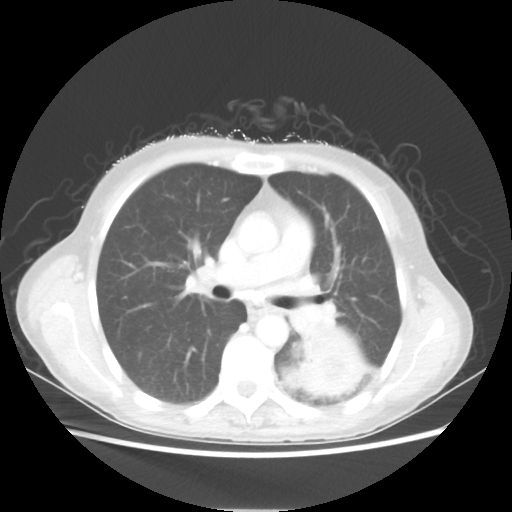
Chest CT, one axial slice. Slice 33 of 56 in the series (ordered by position). Reconstruction kernel STANDARD. 80 kVp. Lung window (W 1500 / L -600 HU). 5 mm slice thickness. 512 × 512 image matrix, field of view 360 × 360 mm. Female patient, age 53 years. Case-level facts recorded for this patient, not image findings: clinical TNM (as recorded): T3 N0 M0.
Annotated regions visible in this slice (bounding box drawn by a radiologist):
- lung tumour (recorded histology: adenocarcinoma): box from (x=276, y=323) to (x=373, y=398) px